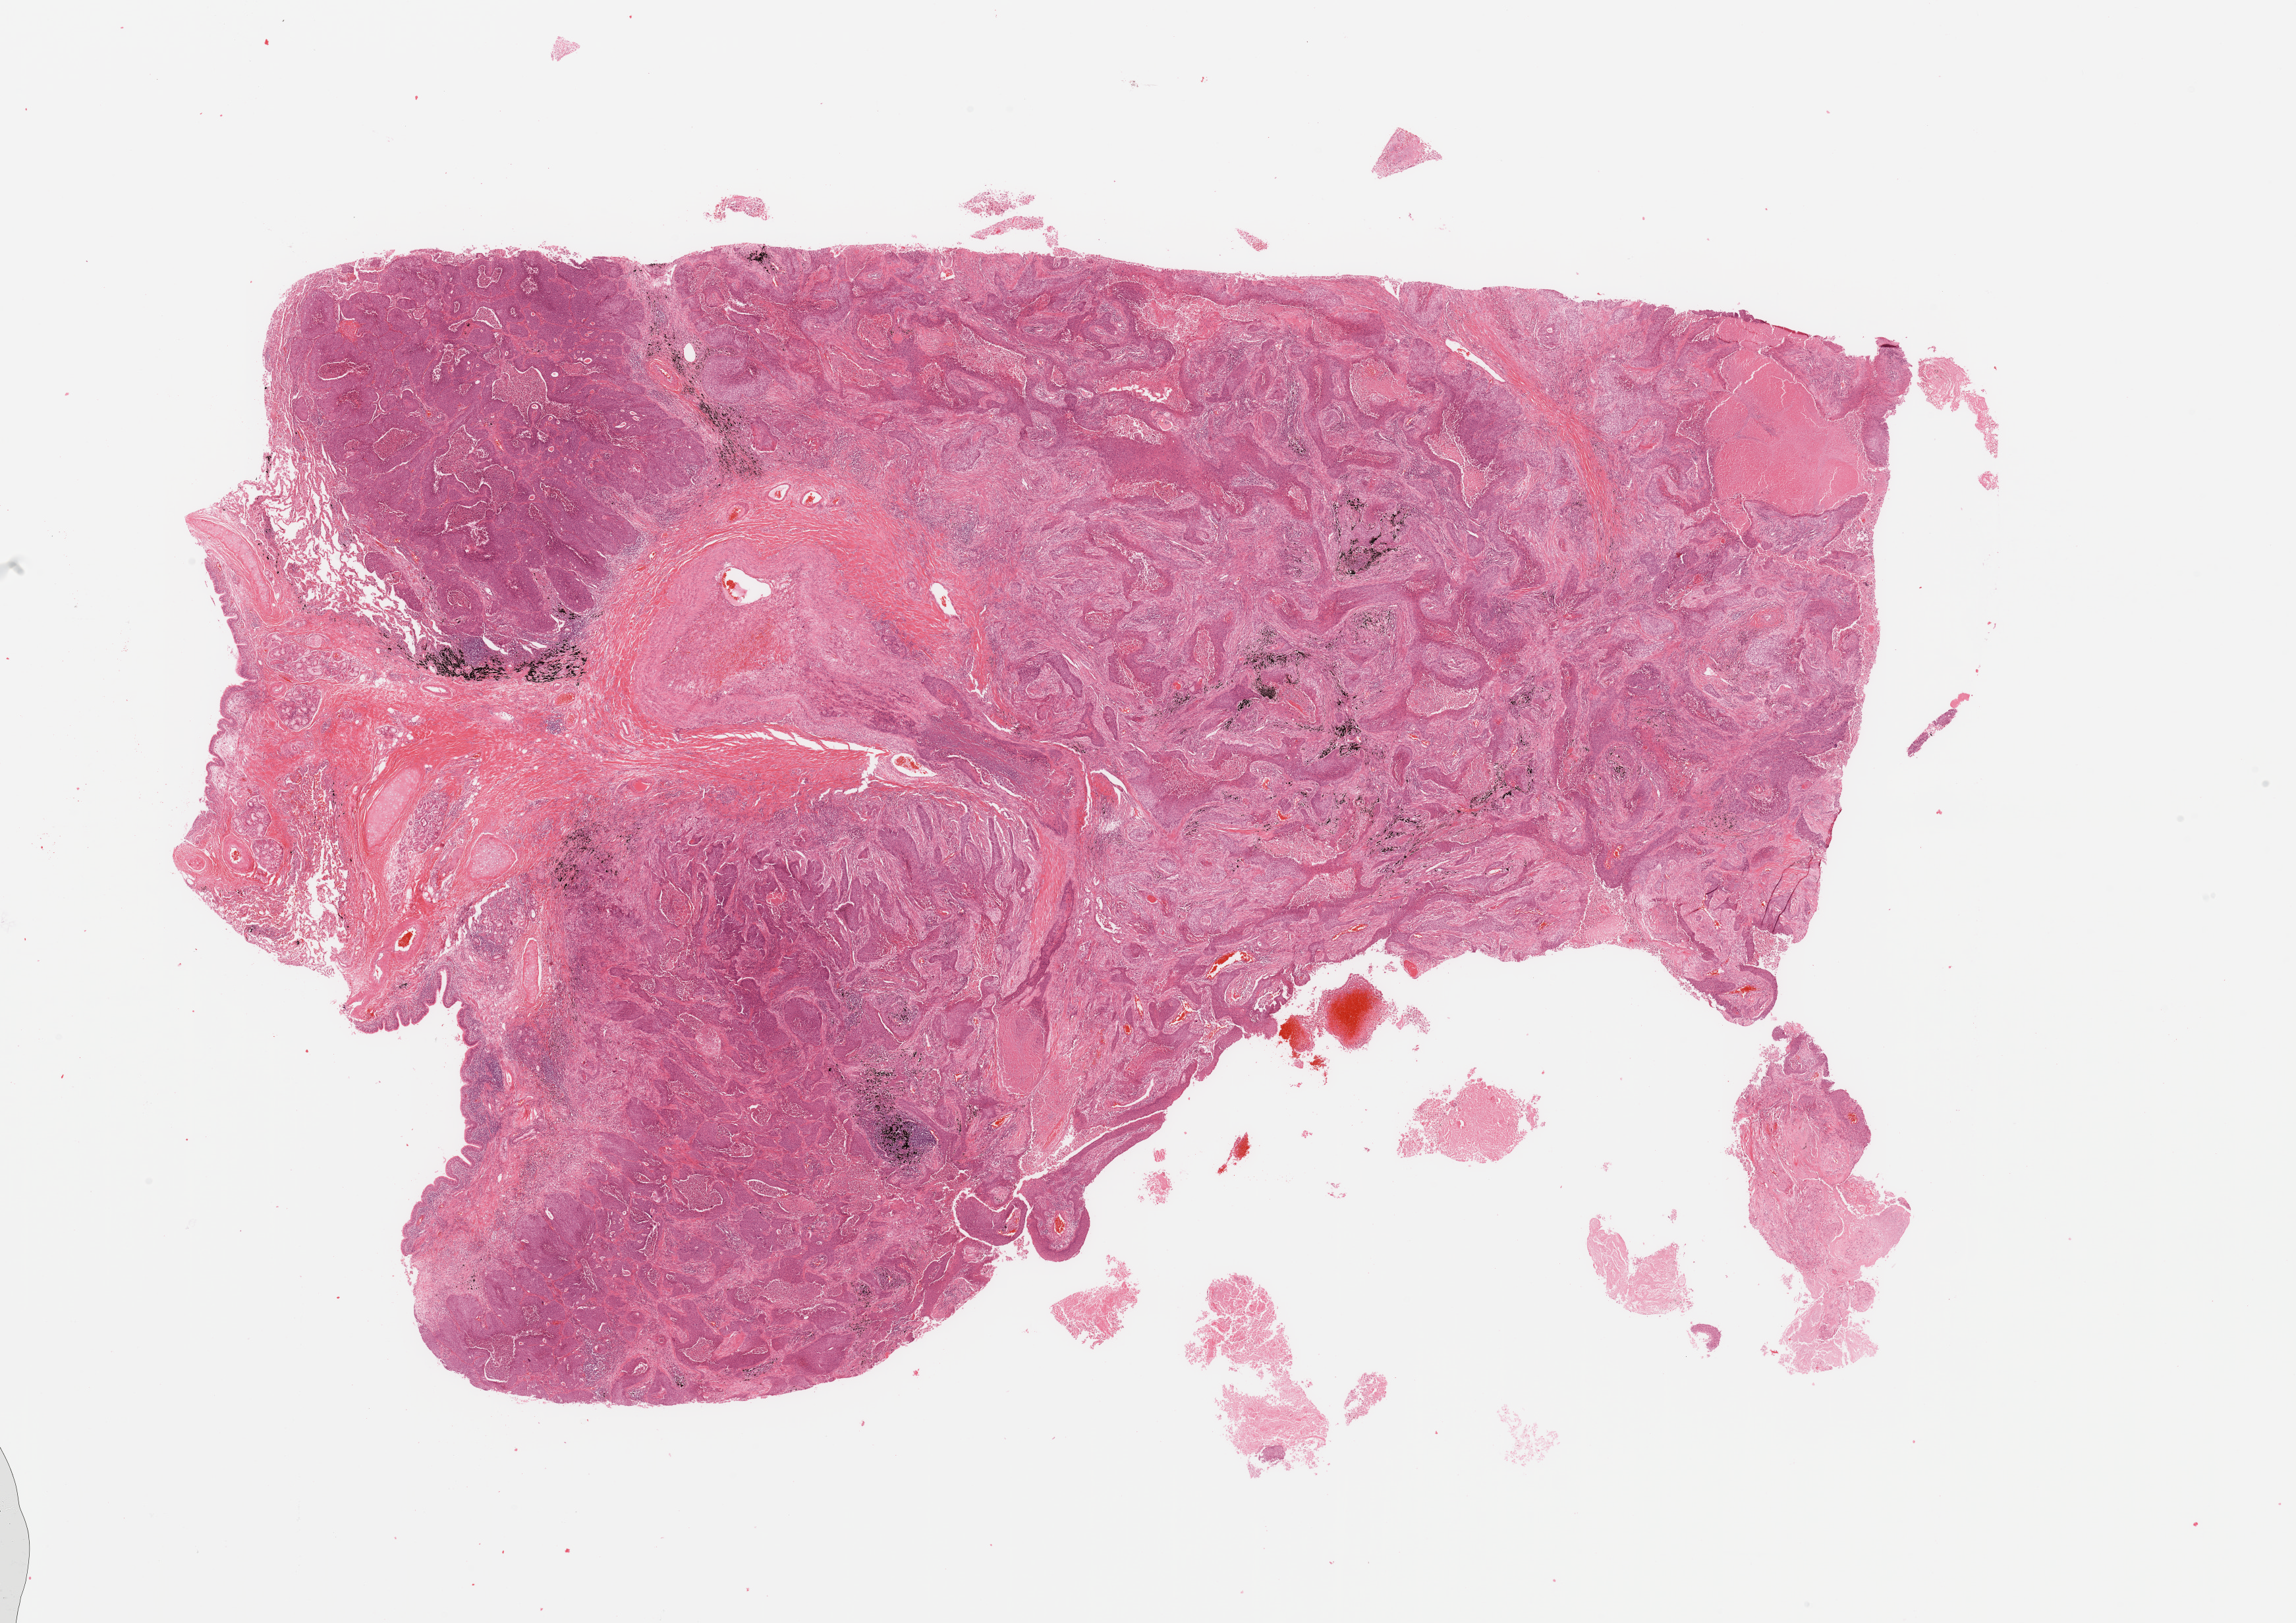
Whole-slide histology image, Hematoxylin and eosin (H&E) stained — a low-resolution overview of the entire scanned area, about 27.6 x 19.5 mm (from a 20x scan), tumour tissue sample, lung. 72-year-old male patient.
Diagnosis: Squamous cell carcinoma, NOS.